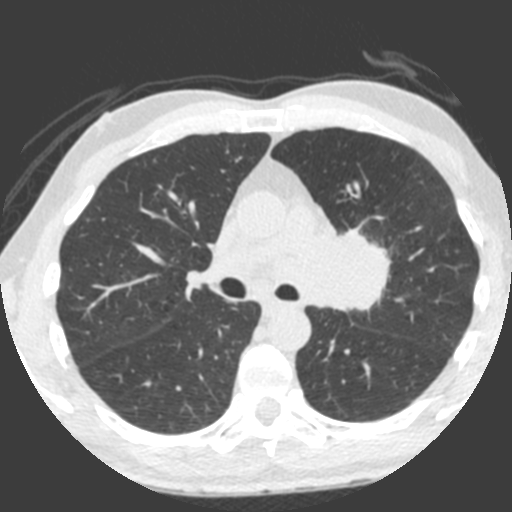
Low-dose screening chest CT, one axial slice. Position 137 of 212 along the scan axis. 120 kVp. Lung window (W 1500 / L -600 HU). 2 mm slice thickness. 512 × 512 image matrix, field of view 315 × 315 mm.
Annotated regions visible in this slice (expert manual segmentation):
- lesion 1 (tumor, upper lobe of left lung): bounding box [x1, y1, x2, y2] px = [321, 228, 390, 312]